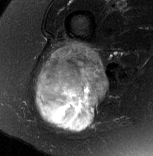
MRI of an extremity soft-tissue mass, one axial slice. Slice 46 of 77 in the series (ordered by position). T2-weighted fat-saturated. MR volume resampled by the dataset authors to the PET/CT grid (not the native acquisition matrix). 3.27 mm slice thickness. 153 × 156 image matrix. Female patient. Case-level facts recorded for this patient, not image findings: histological type: synovial sarcoma; grade: intermediate; site of the primary tumour: right buttock.
Annotated regions visible in this slice (expert contour drawn on MRI and transferred to this co-registered scan by the dataset authors):
- gross tumour volume including surrounding oedema: box from (x=35, y=43) to (x=109, y=133) px
- gross tumour volume (mass): (x=35, y=43)–(x=109, y=130)